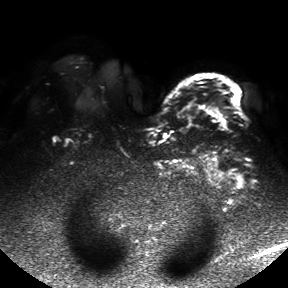
Breast MRI, one axial slice; diffusion-weighted series; image 2 of 4 stored at this slice position (different b-values; order by instance number); 1.5 T; 4 mm slice thickness; 288 × 288 image matrix, field of view 390 × 390 mm. Female patient.
Outlined on this slice (manually delineated by an expert):
- tumour on diffusion-weighted imaging: bounding box <210,111,228,129> (left, top, right, bottom; pixels)